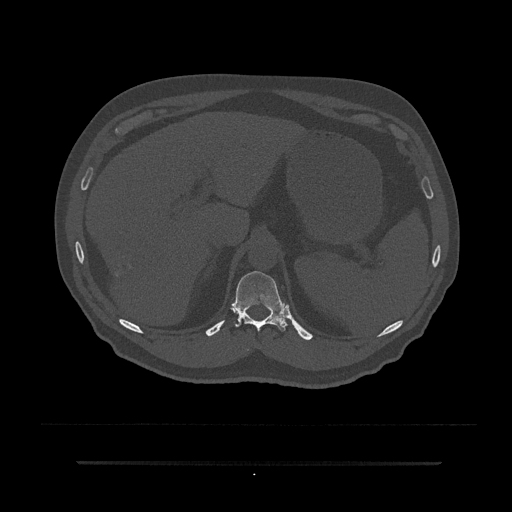
CT including the spine, one axial slice; position 270 of 797 along the scan axis; 120 kVp; bone window (W 1800 / L 400 HU); 0.5 mm slice thickness; 512 × 512 image matrix, field of view 464 × 464 mm. Patient: male, 59 years. Case-level facts recorded for this patient, not image findings: primary cancer: bile ducts; vertebrae with lytic lesions (as recorded): T10.
Structures marked on this image (semi-automatically segmented with operator editing):
- T11 vertebra: bounding box (x1, y1, x2, y2) in pixels: (233, 271, 288, 332)